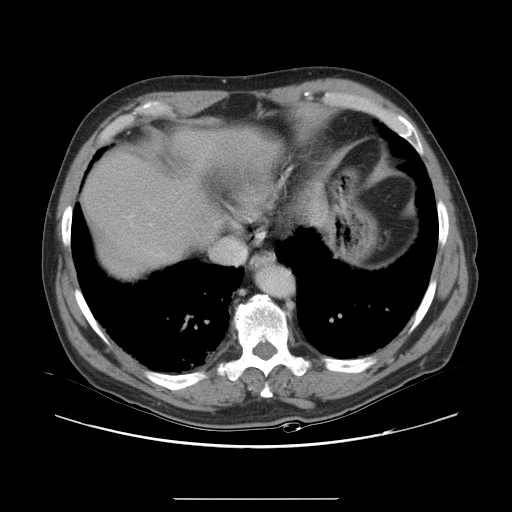
Contrast-enhanced abdominal CT, one axial slice. Position 29 of 40 along the scan axis. Intravenous contrast given. Soft-tissue window (W 400 / L 40 HU). 512 × 512 image matrix, field of view 408 × 408 mm. Male patient, age 64 years. Case-level facts recorded for this patient, not image findings: diagnosis: colorectal cancer liver metastases, imaged before liver resection; multiple liver metastases: yes; largest metastasis: 3.2 cm; chemotherapy before resection: yes.
Annotated regions visible in this slice (expert manual segmentation):
- hepatic veins: bounding box (x1, y1, x2, y2) in pixels: (157, 253, 164, 257)
- liver: (85, 131, 270, 276)
- planned liver remnant (the part of the liver to remain after resection): (85, 131, 270, 265)